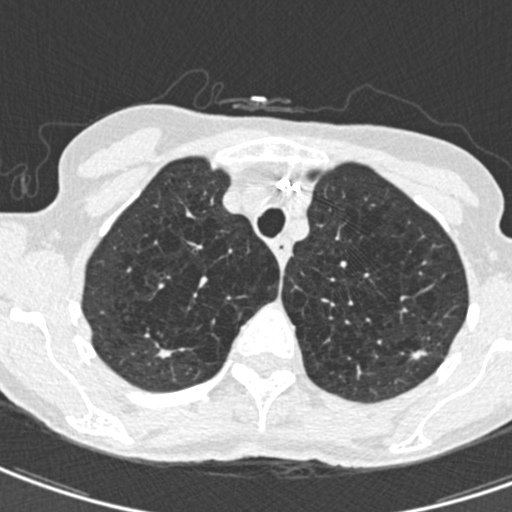
Chest CT (low-dose screening protocol), one axial image; second screening round (one year after baseline); lung window (W 1500 / L -600 HU); slice 107 of 498 in the series; 512 × 512 image matrix. Female, age 71 years at enrolment. Current smoker at enrolment.
- Expert reader's lesion annotation, bounding box <405,332,444,370> (left, top, right, bottom; pixels).
- The screening reader recorded 2 non-calcified nodules or masses ≥4 mm on this exam (right upper lobe, left upper lobe); which of them this box marks is not recorded.
- Official screen result: positive, change unspecified: nodule(s) >= 4 mm or enlarging nodule(s), mass(es), or other non-specific abnormalities suspicious for lung cancer.
- Lung cancer was diagnosed 604 days after this screen (after the third annual screen): adenocarcinoma, NOS, left upper lobe, moderately differentiated (G2), stage IA (AJCC 6th edition), 12 mm at pathology.